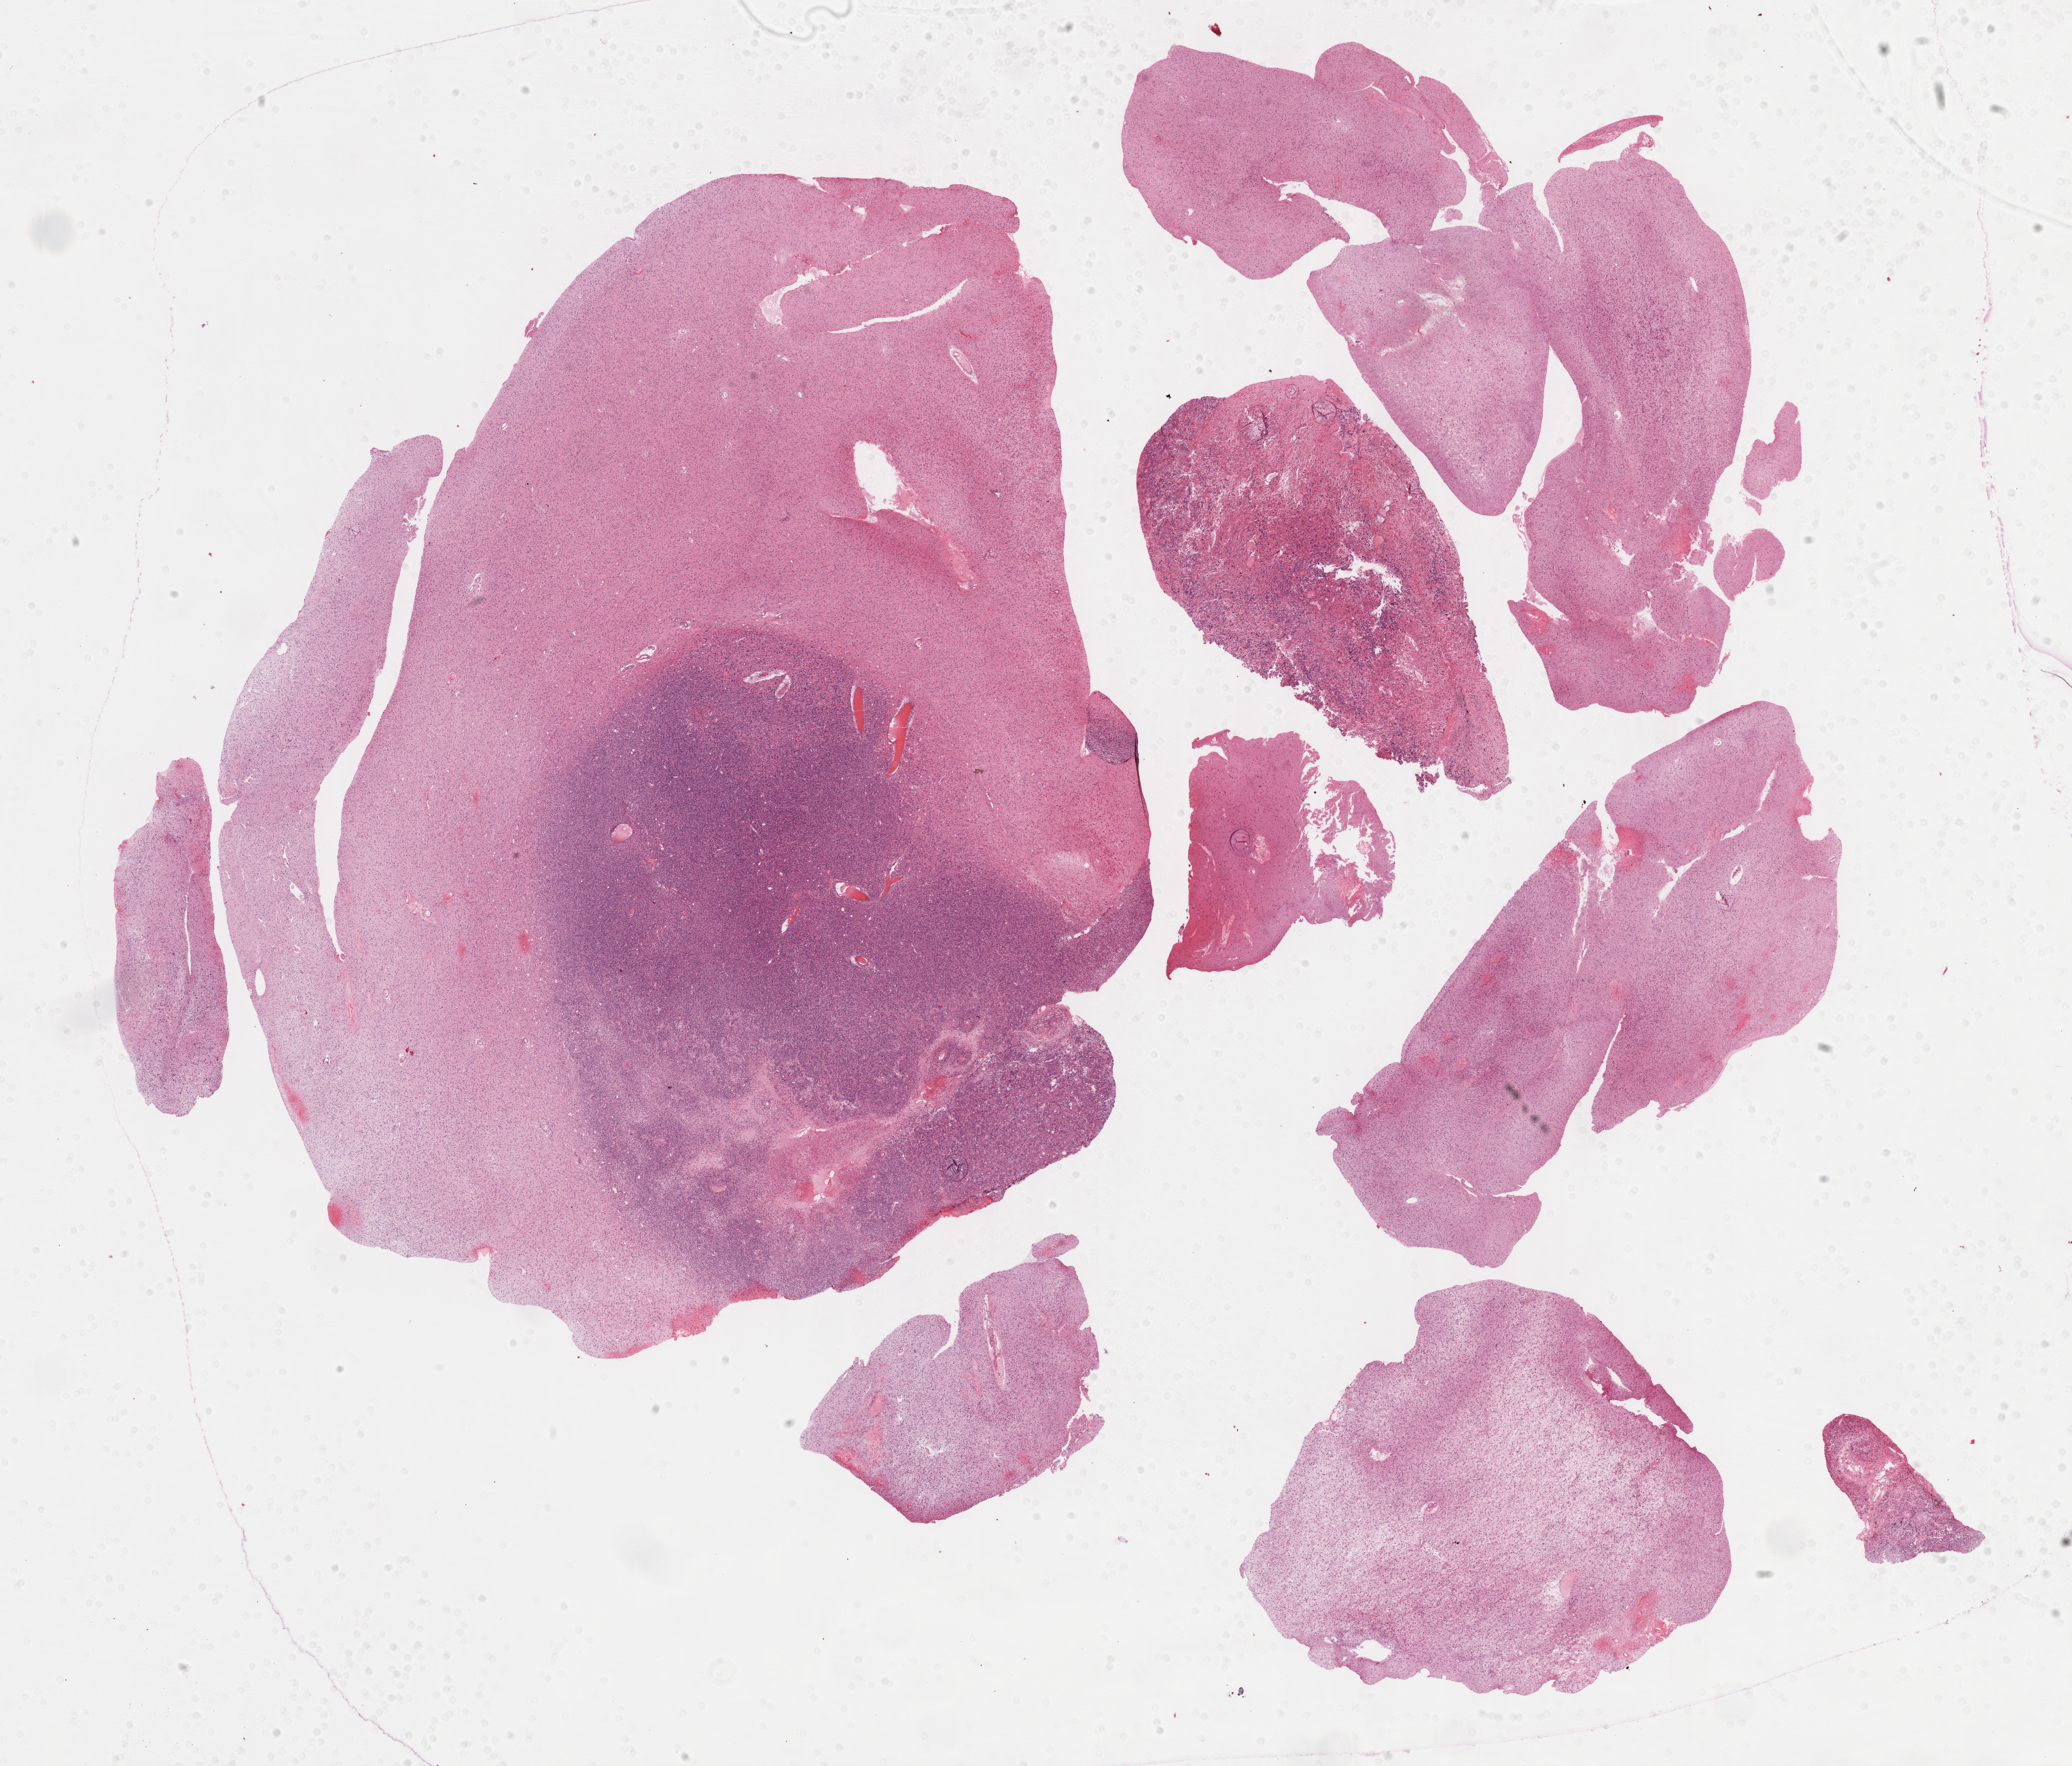
Hematoxylin and eosin (H&E) stained whole-slide image — a low-resolution overview of the entire scanned area, about 24.7 x 21.0 mm (acquisition: 40x scan). Formalin-fixed paraffin-embedded (FFPE) diagnostic section. Primary tumour sample from the brain. Patient: male, age at initial diagnosis 34 years.
Histologic diagnosis: Glioblastoma.